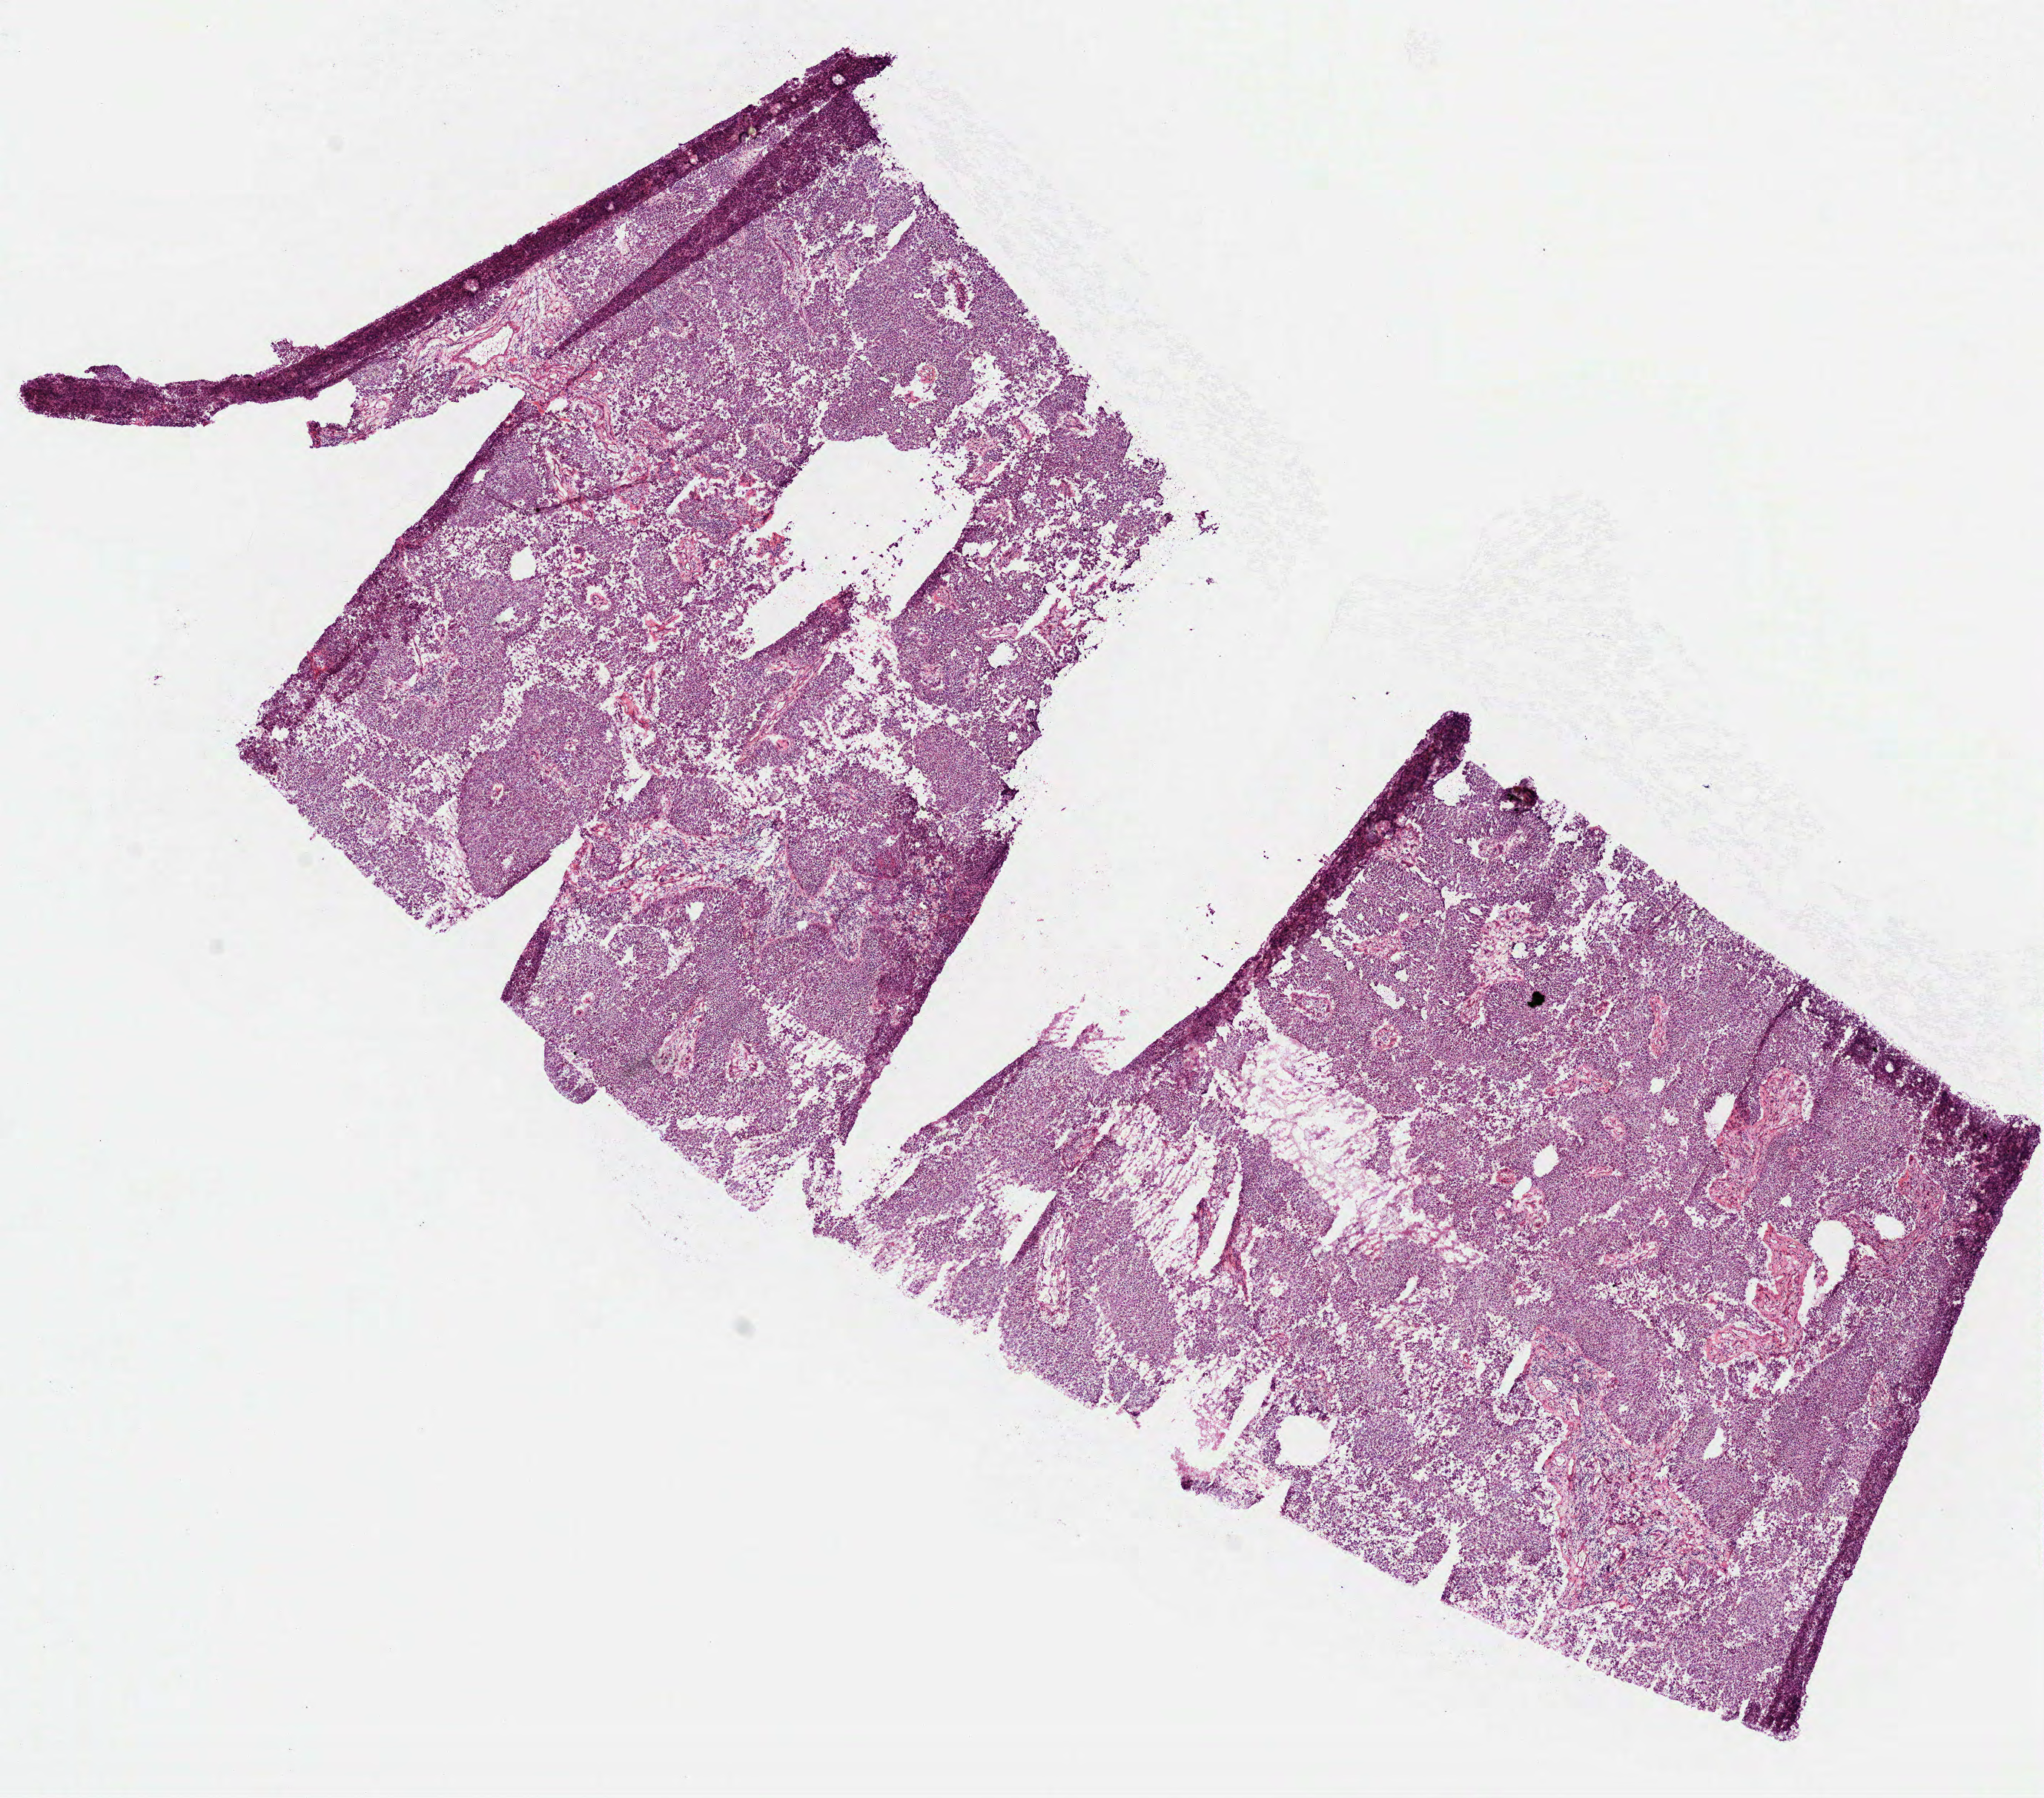
Digitized H&E-stained tissue section (whole slide) — low-resolution overview of the scanned area, about 11.1 x 9.8 mm (slide scanned at 40x); frozen section from the top of the tissue portion; kidney, primary tumour sample. Patient sex: female.
Diagnosis: Papillary adenocarcinoma, NOS.